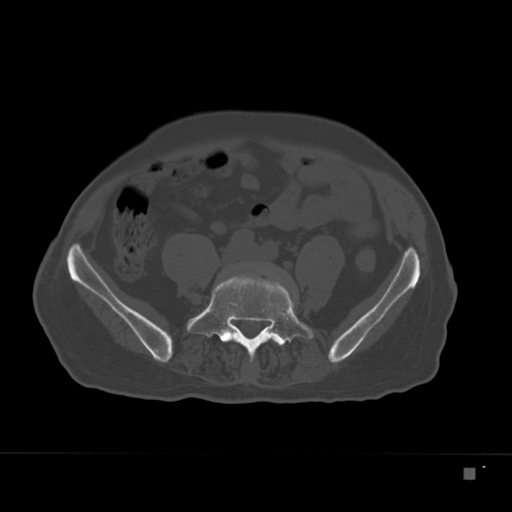
CT including the spine, one axial slice. Slice 27 of 332 in the series (ordered by position). Reconstruction kernel Br40s. 120 kVp. Bone window (W 1800 / L 400 HU). 512 × 512 image matrix, field of view 389 × 389 mm. Male patient, age 72 years. From the clinical record (not read from this slice): primary cancer: skeletal.
Annotated regions visible in this slice (semi-automatically segmented with operator editing):
- L4 vertebra: bounding box [x1, y1, x2, y2] px = [249, 341, 279, 362]
- L5 vertebra: [192, 276, 313, 362]